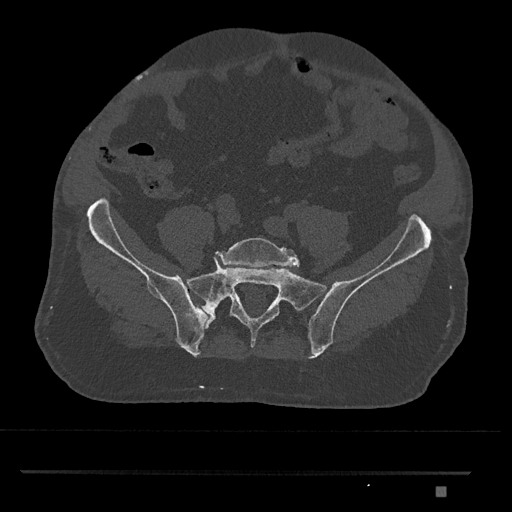
CT including the spine, one axial slice; reconstruction kernel Br40s/3; 120 kVp; bone window (W 1800 / L 400 HU); 0.5 mm slice thickness; 512 × 512 image matrix, field of view 429 × 429 mm. Patient: male, 65 years. From the clinical record (not read from this slice): primary cancer: prostate.
Annotated regions visible in this slice (semi-automatically segmented with operator editing):
- L5 vertebra: bounding box (x1, y1, x2, y2) in pixels: (215, 237, 300, 268)